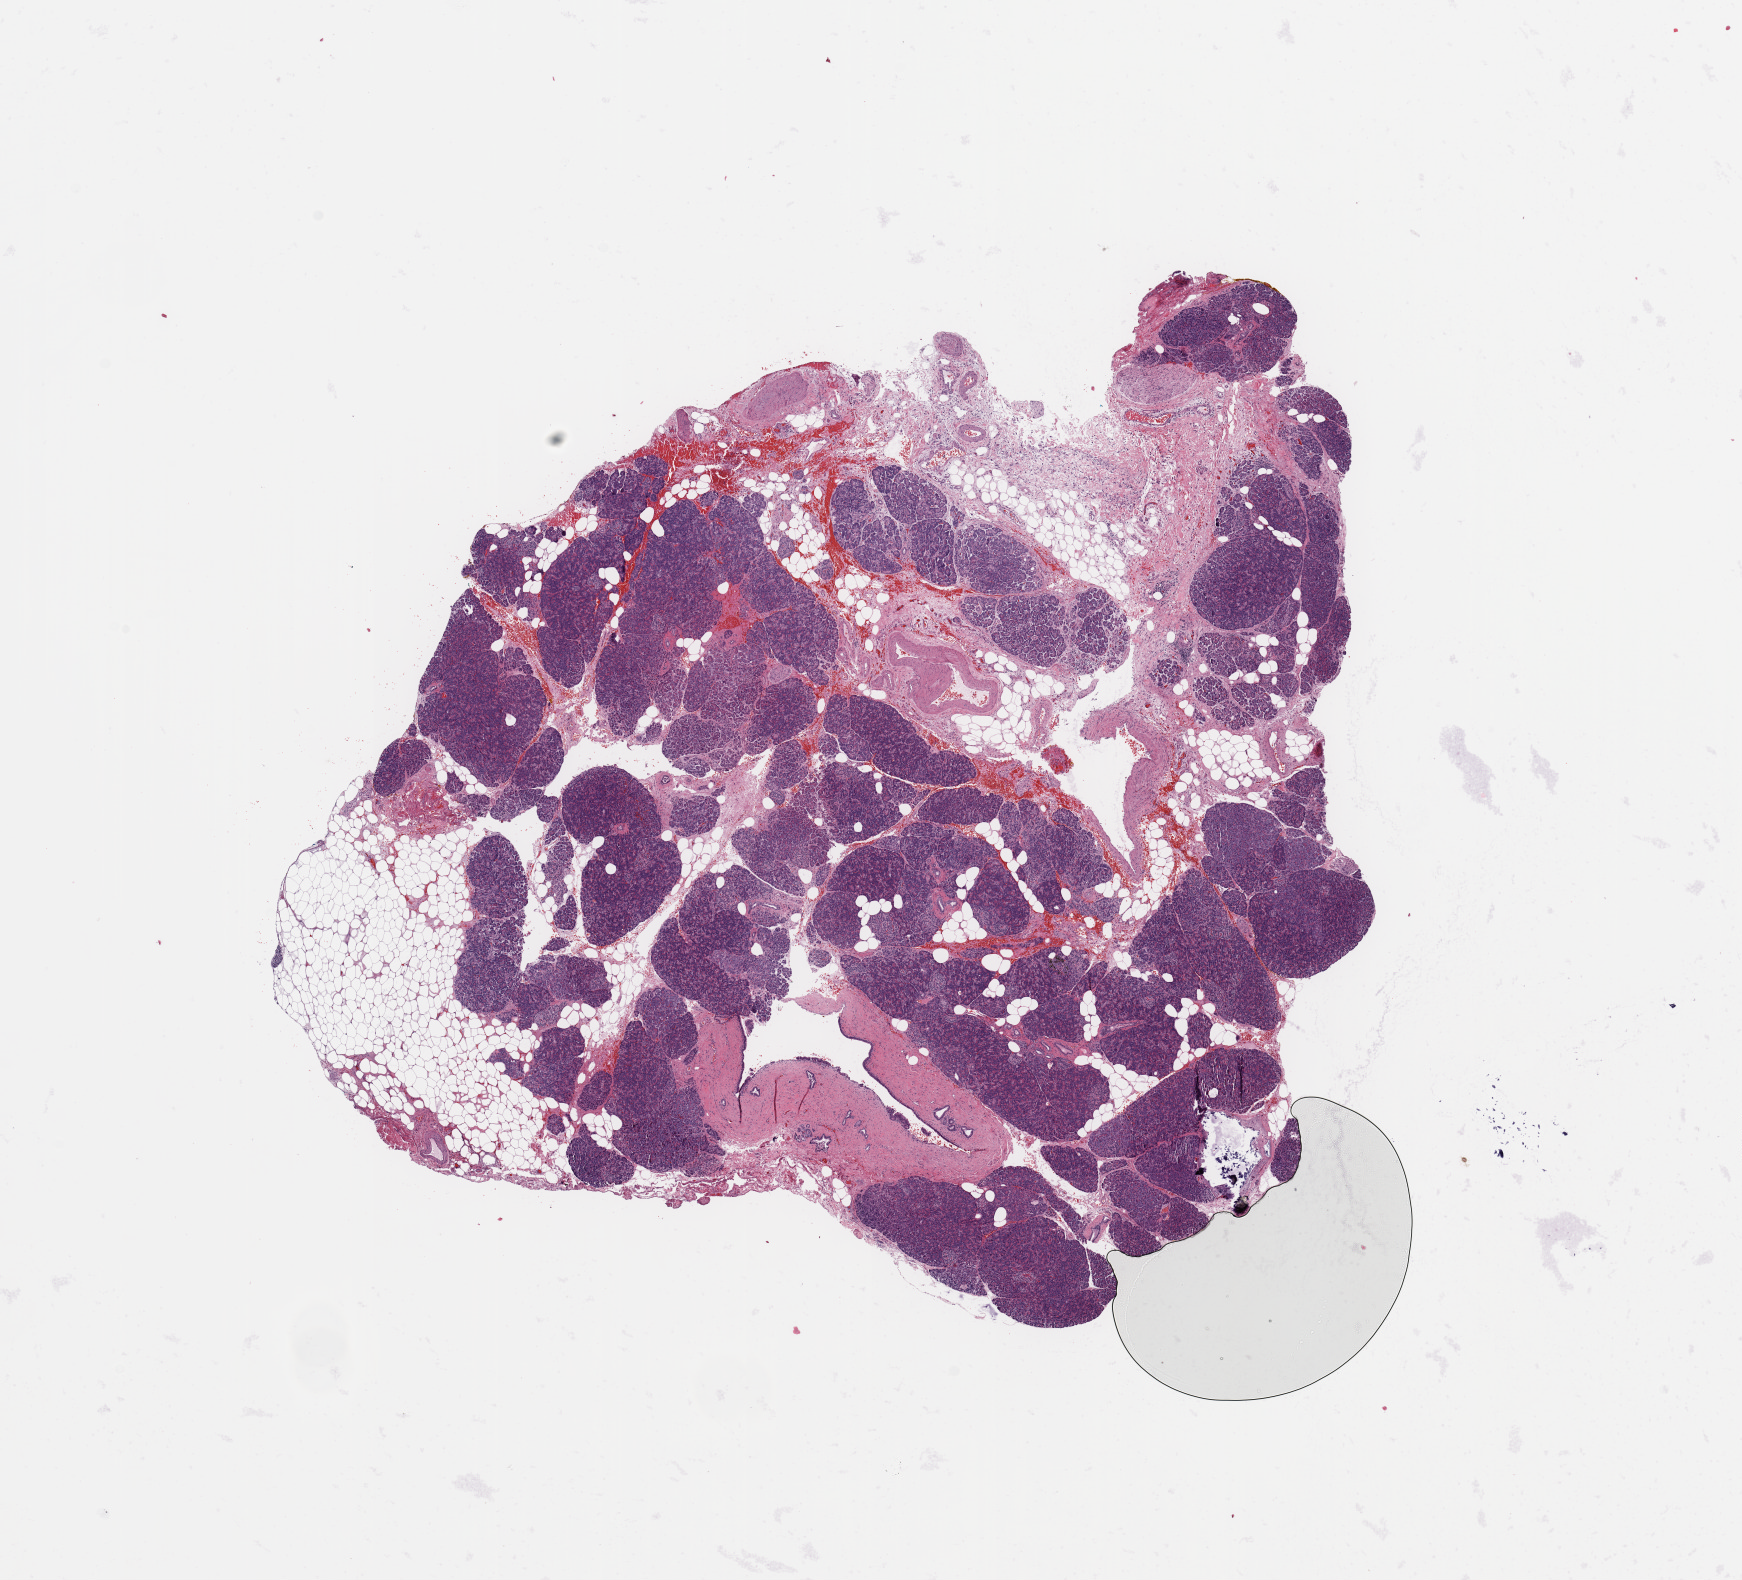
Digitized Hematoxylin and eosin (H&E) stained tissue section (whole slide), a low-resolution overview of the entire scanned area, about 13.8 x 12.5 mm (acquisition: 20x scan), pancreas, normal (non-tumour) tissue. 81-year-old male patient.
This section: normal (non-tumour) tissue from the same patient. Patient diagnosis: Infiltrating duct carcinoma, NOS.